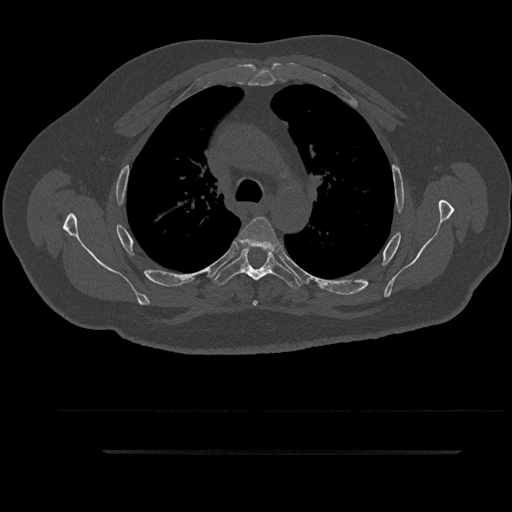
CT including the spine, one axial slice. Slice 646 of 797 in the series (ordered by position). Reconstruction kernel Br40s/3. 120 kVp. Bone window (W 1800 / L 400 HU). 0.5 mm slice thickness. 512 × 512 image matrix, field of view 432 × 432 mm. Patient: male, 63 years. From the clinical record (not read from this slice): primary cancer: renal.
Annotated regions visible in this slice (semi-automatic segmentation, software-assisted and operator-edited):
- T4 vertebra: bounding box <237,216,281,306> (left, top, right, bottom; pixels)
- T5 vertebra: <214,246,300,290>